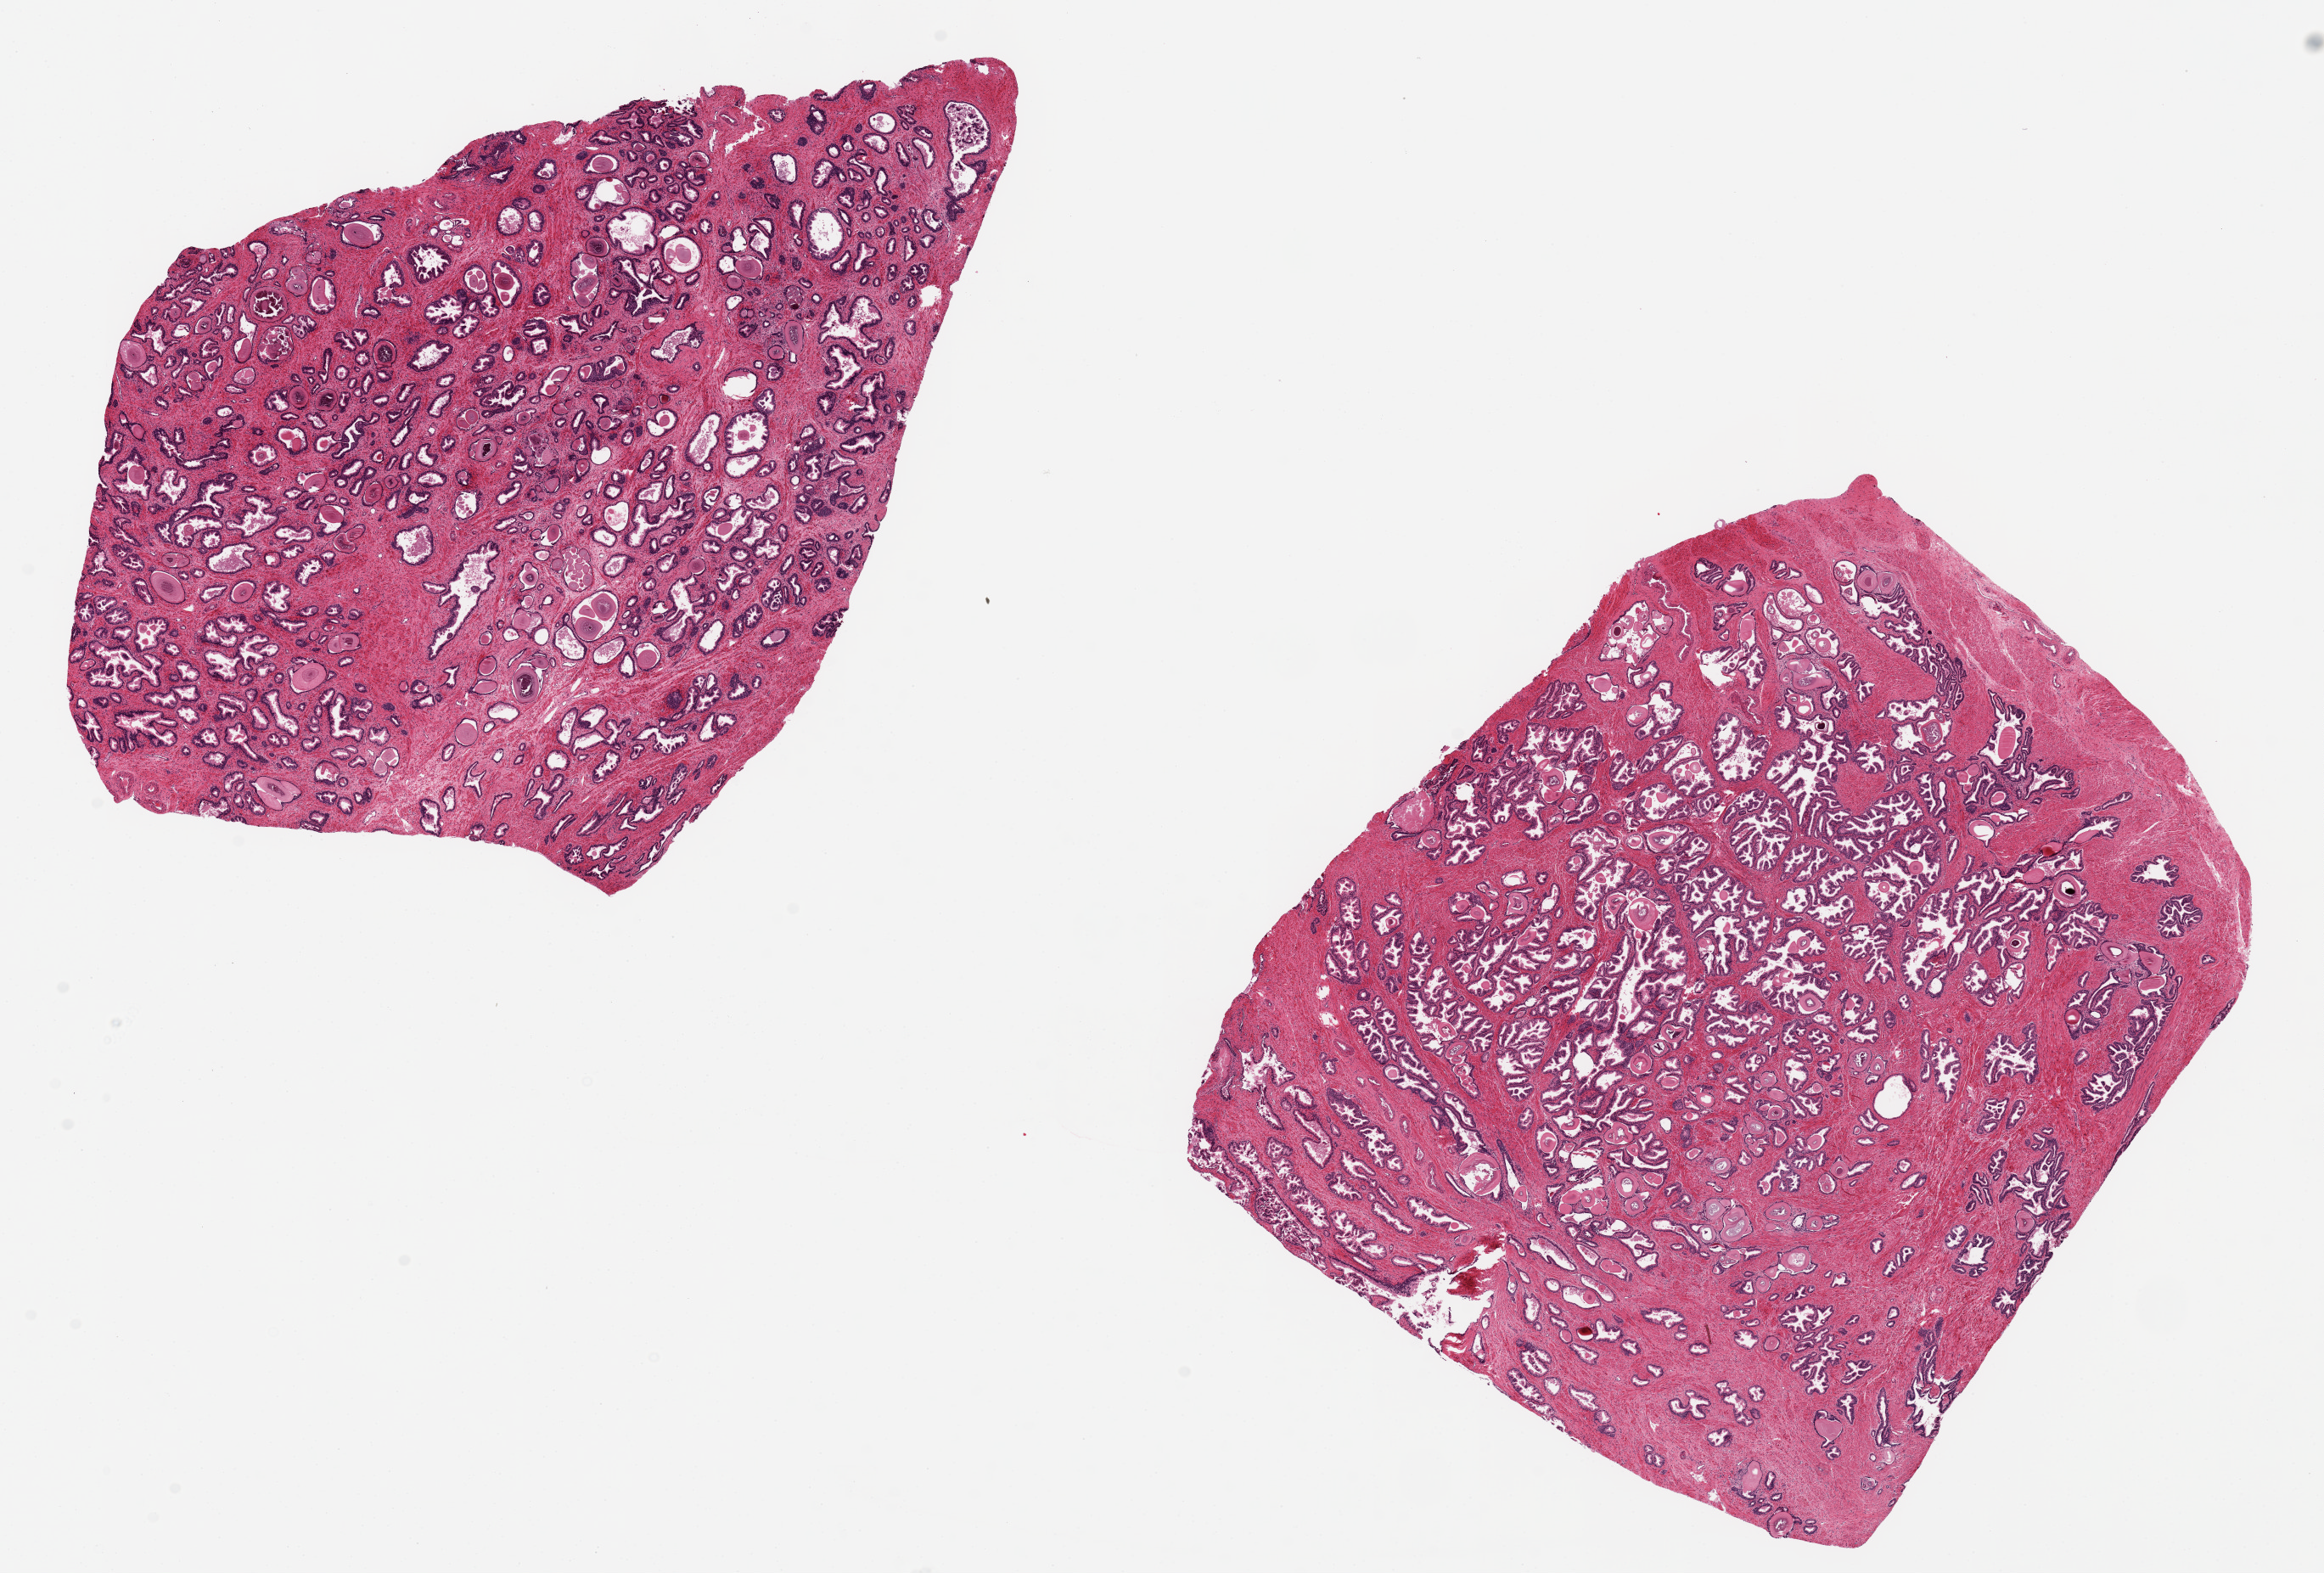
Whole-slide image, hematoxylin and eosin (H&E) stain, brightfield, whole scanned area (about 21.7 x 14.7 mm) shown as a low-resolution overview, PAXgene-fixed paraffin-embedded (PFPE) section, sampled site (target tissue): prostate, donor tissue sample.
* pathologist's review note for this sample: 2 ~8.5x6.5mm pieces. Glandular and stromal hyperplasia